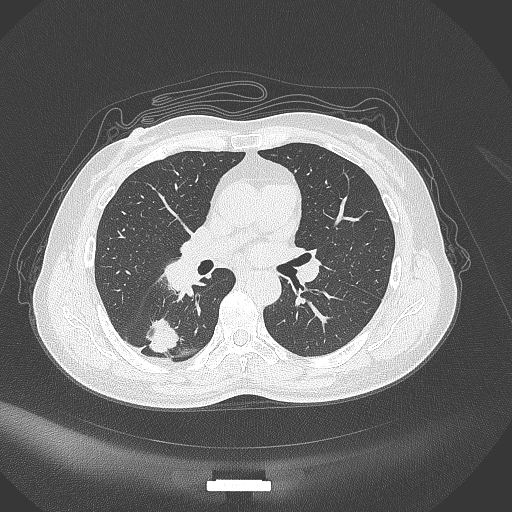
Chest CT, one axial slice; slice 167 of 352 in the series (ordered by position); reconstruction kernel B70f; lung window (W 1500 / L -600 HU); 1 mm slice thickness; 512 × 512 image matrix, field of view 400 × 400 mm. Female patient, age 55 years. From the clinical record (not read from this slice): clinical TNM (as recorded): T1c N1 M0.
Annotated regions visible in this slice (bounding box drawn by a radiologist):
- lung tumour (recorded histology: adenocarcinoma): bounding box [x1, y1, x2, y2] px = [142, 315, 184, 361]